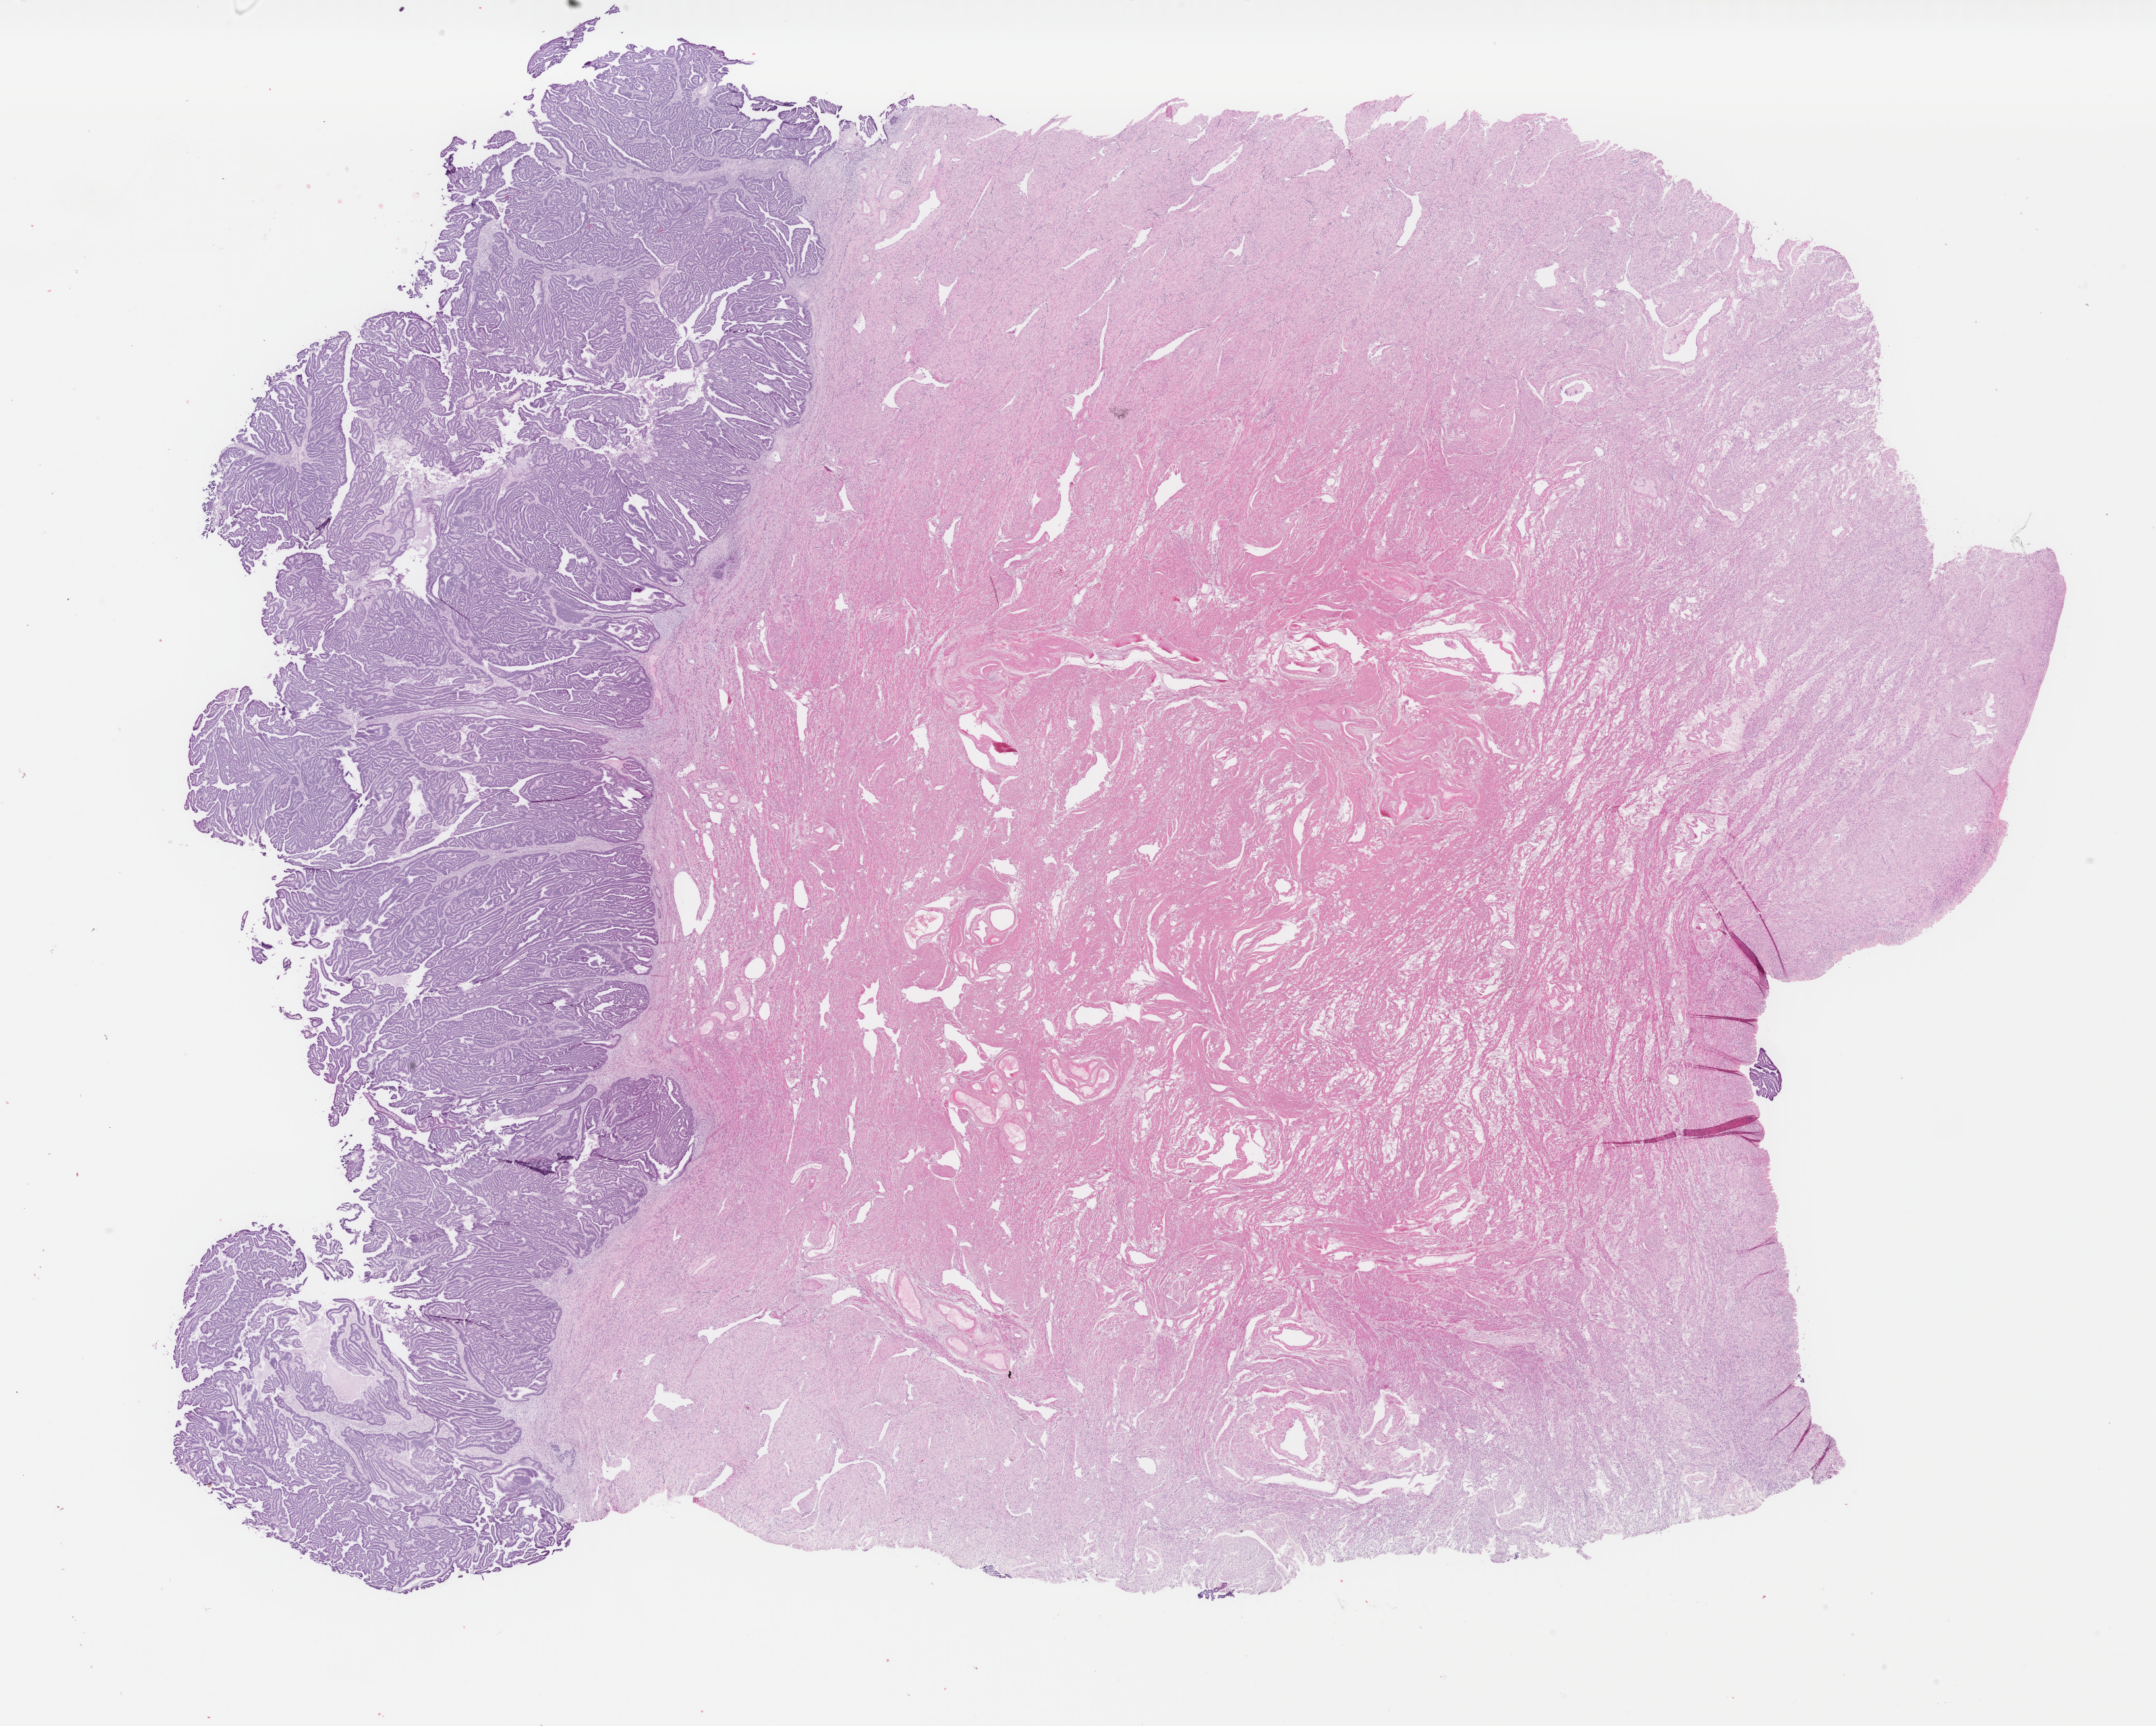
Digitized Hematoxylin and eosin (H&E) stained tissue section (whole slide), shown as a low-resolution overview of the whole scanned area (about 26.0 x 20.8 mm); formalin-fixed paraffin-embedded (FFPE) diagnostic section; primary tumour sample from the uterus. Female, age 64 years at initial diagnosis. Histologic grade: G1 (well differentiated).
- FIGO stage: IIIA
- histologic diagnosis: Endometrioid adenocarcinoma, NOS (endometrium)